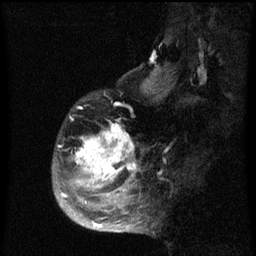
Breast MRI (dynamic contrast-enhanced), one sagittal slice; slice 18 of 60 in the series (ordered by position); dynamic contrast-enhanced series, image 2 of 3 at this slice position (ordered by acquisition); 1.5 T; TE 4.2 ms, TR 8 ms; 2 mm slice thickness; 256 × 256 image matrix, field of view 190 × 190 mm. Patient: female, 50 years.
Structures marked on this image (semi-automatic segmentation, software-assisted and operator-edited):
- analysis volume of interest (the breast-tissue region the enhancement analysis was run in; not a lesion): bounding box [x1, y1, x2, y2] px = [53, 94, 142, 216]
- tumour enhancement mask (voxels above the 70 % enhancement threshold inside the analysis volume of interest): [60, 122, 137, 206]